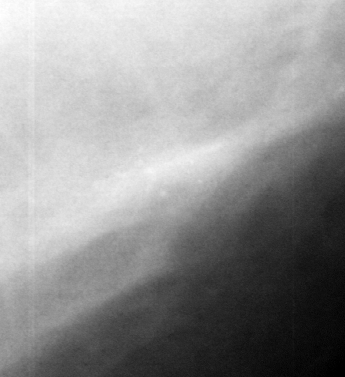
Region of interest cut from a scanned film mammogram (one marked finding); left breast; MLO view.
Finding: calcifications, morphology punctate, distribution clustered; BI-RADS assessment category 4; subtlety rating 3 on a 1 (subtle) to 5 (obvious) scale; pathology result (as recorded, not read from the image): benign.